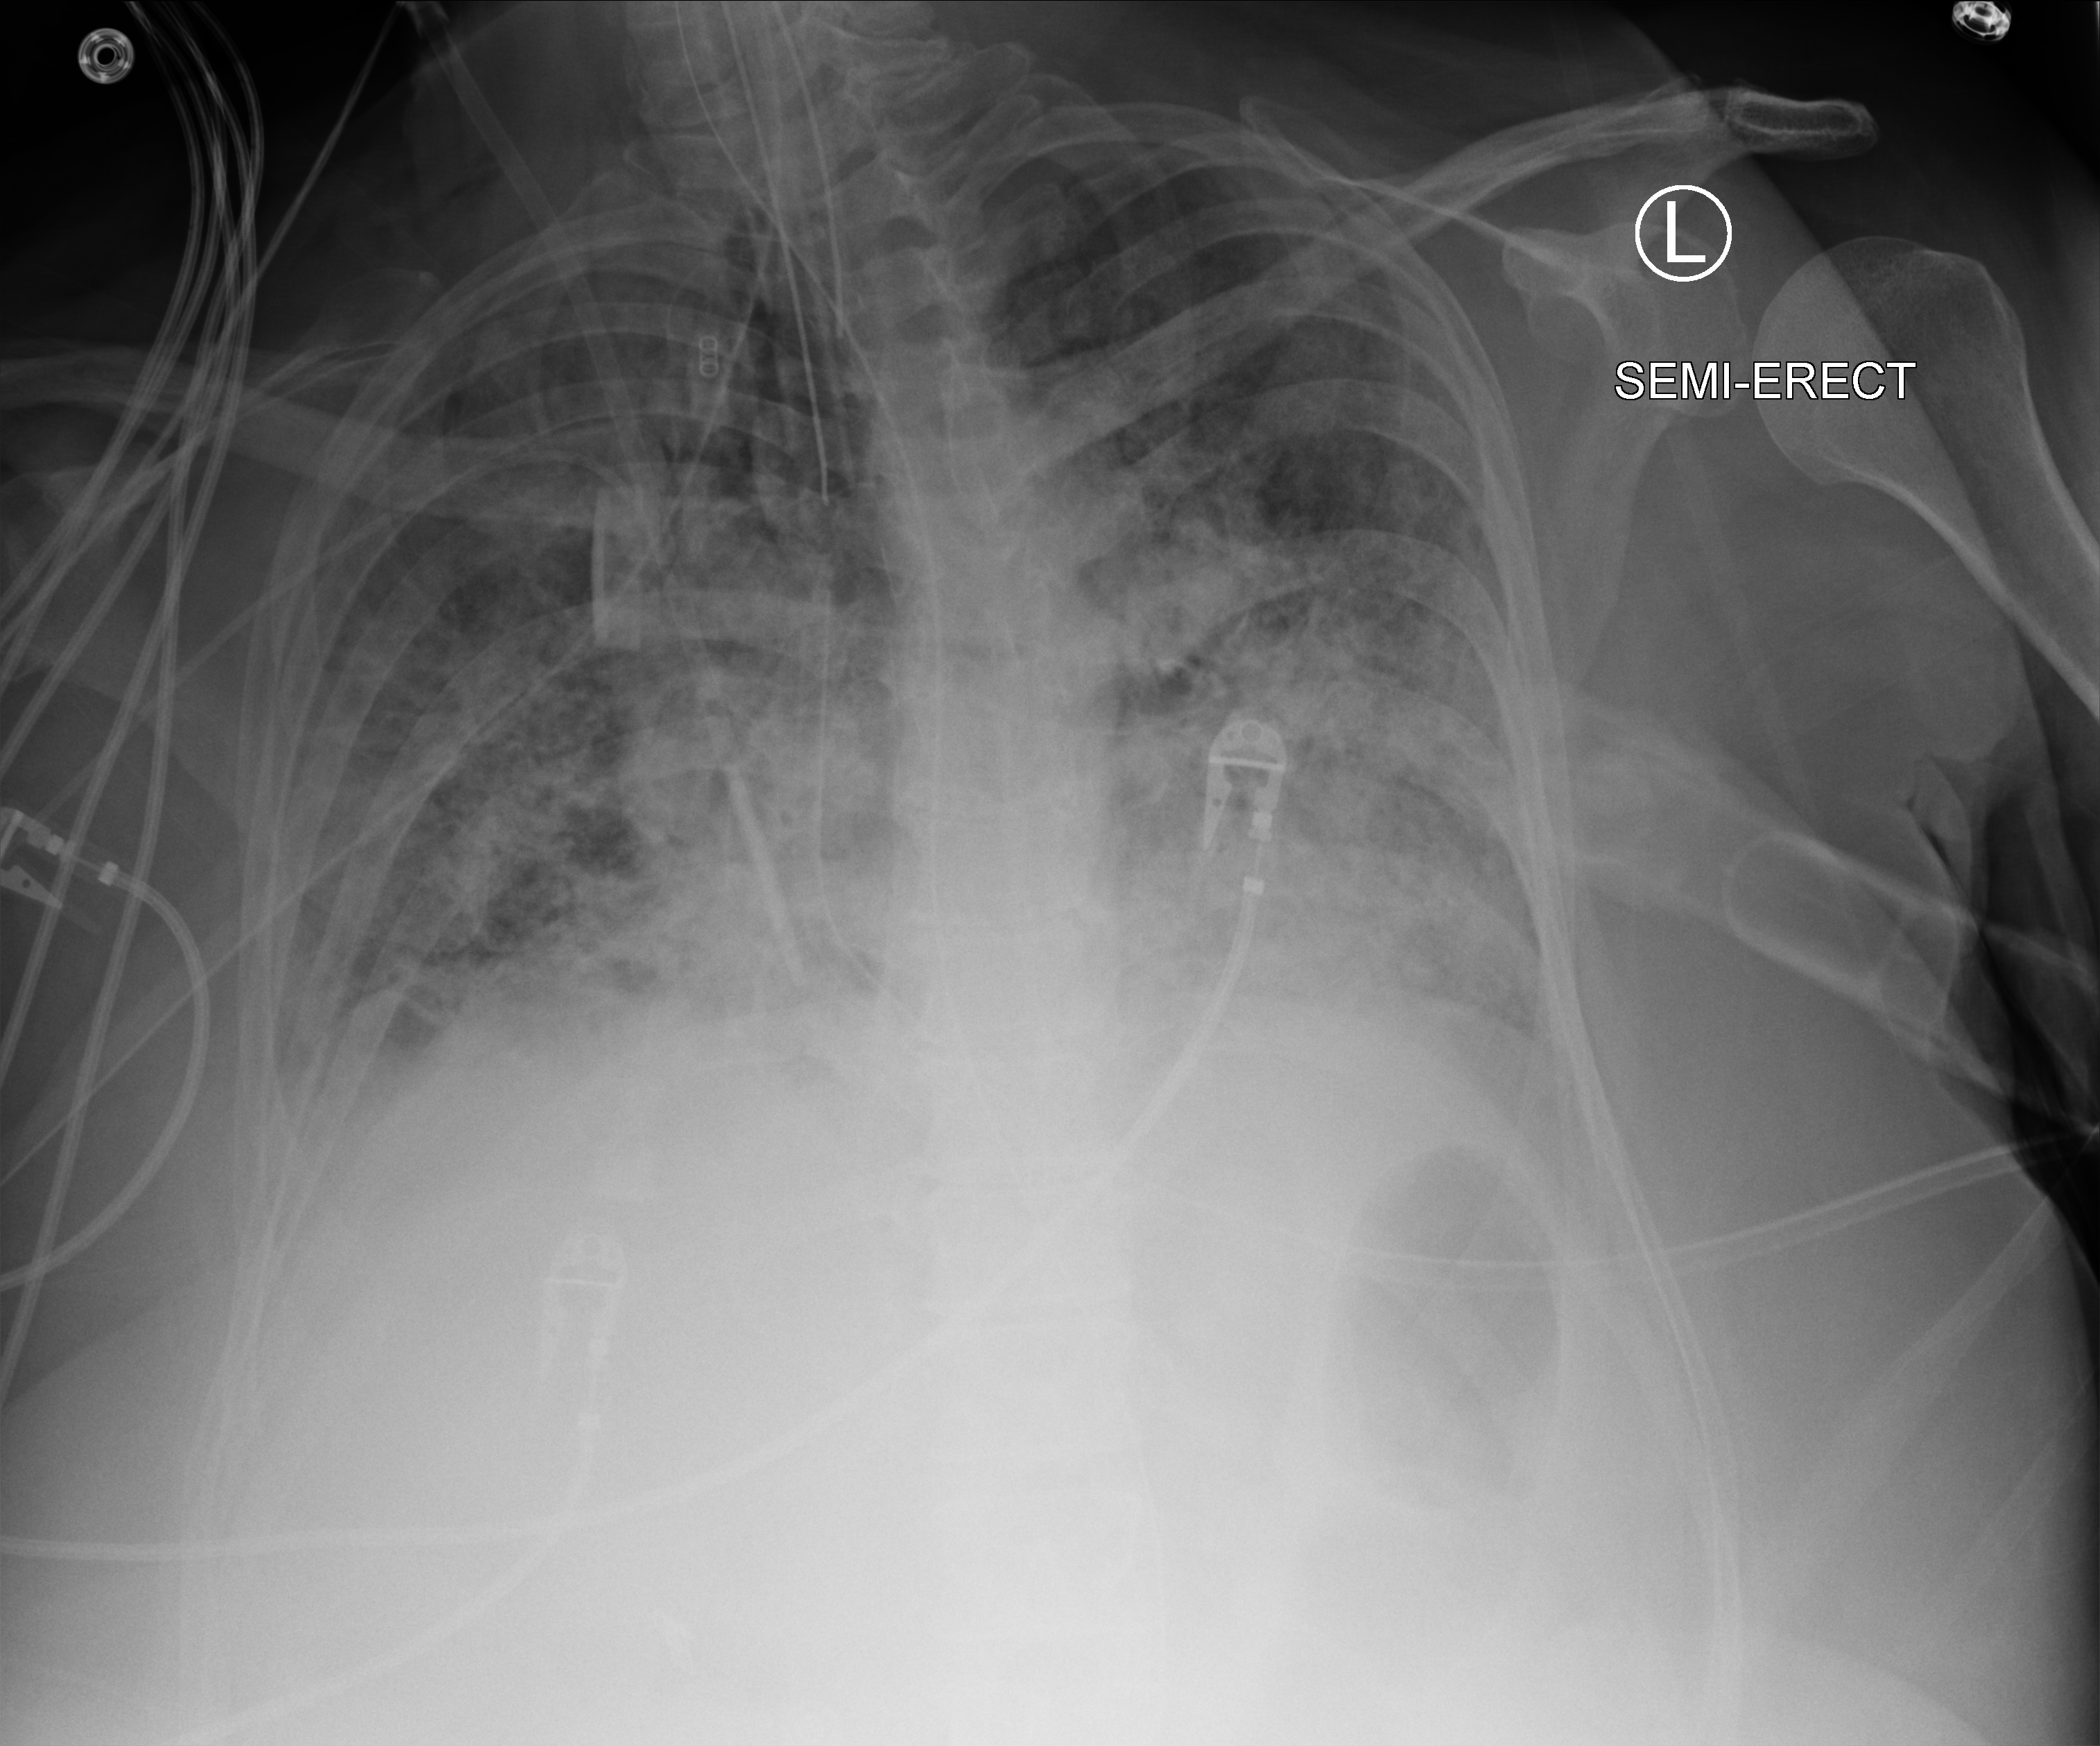
Portable chest radiograph. Patient hospitalised with COVID-19; female, aged 60–74 years.
From the hospital-stay record, not from the radiograph (when in the stay this image was taken is not recorded):
- other chronic lung disease (admission record): yes
- admitted to intensive care during this hospital stay: yes